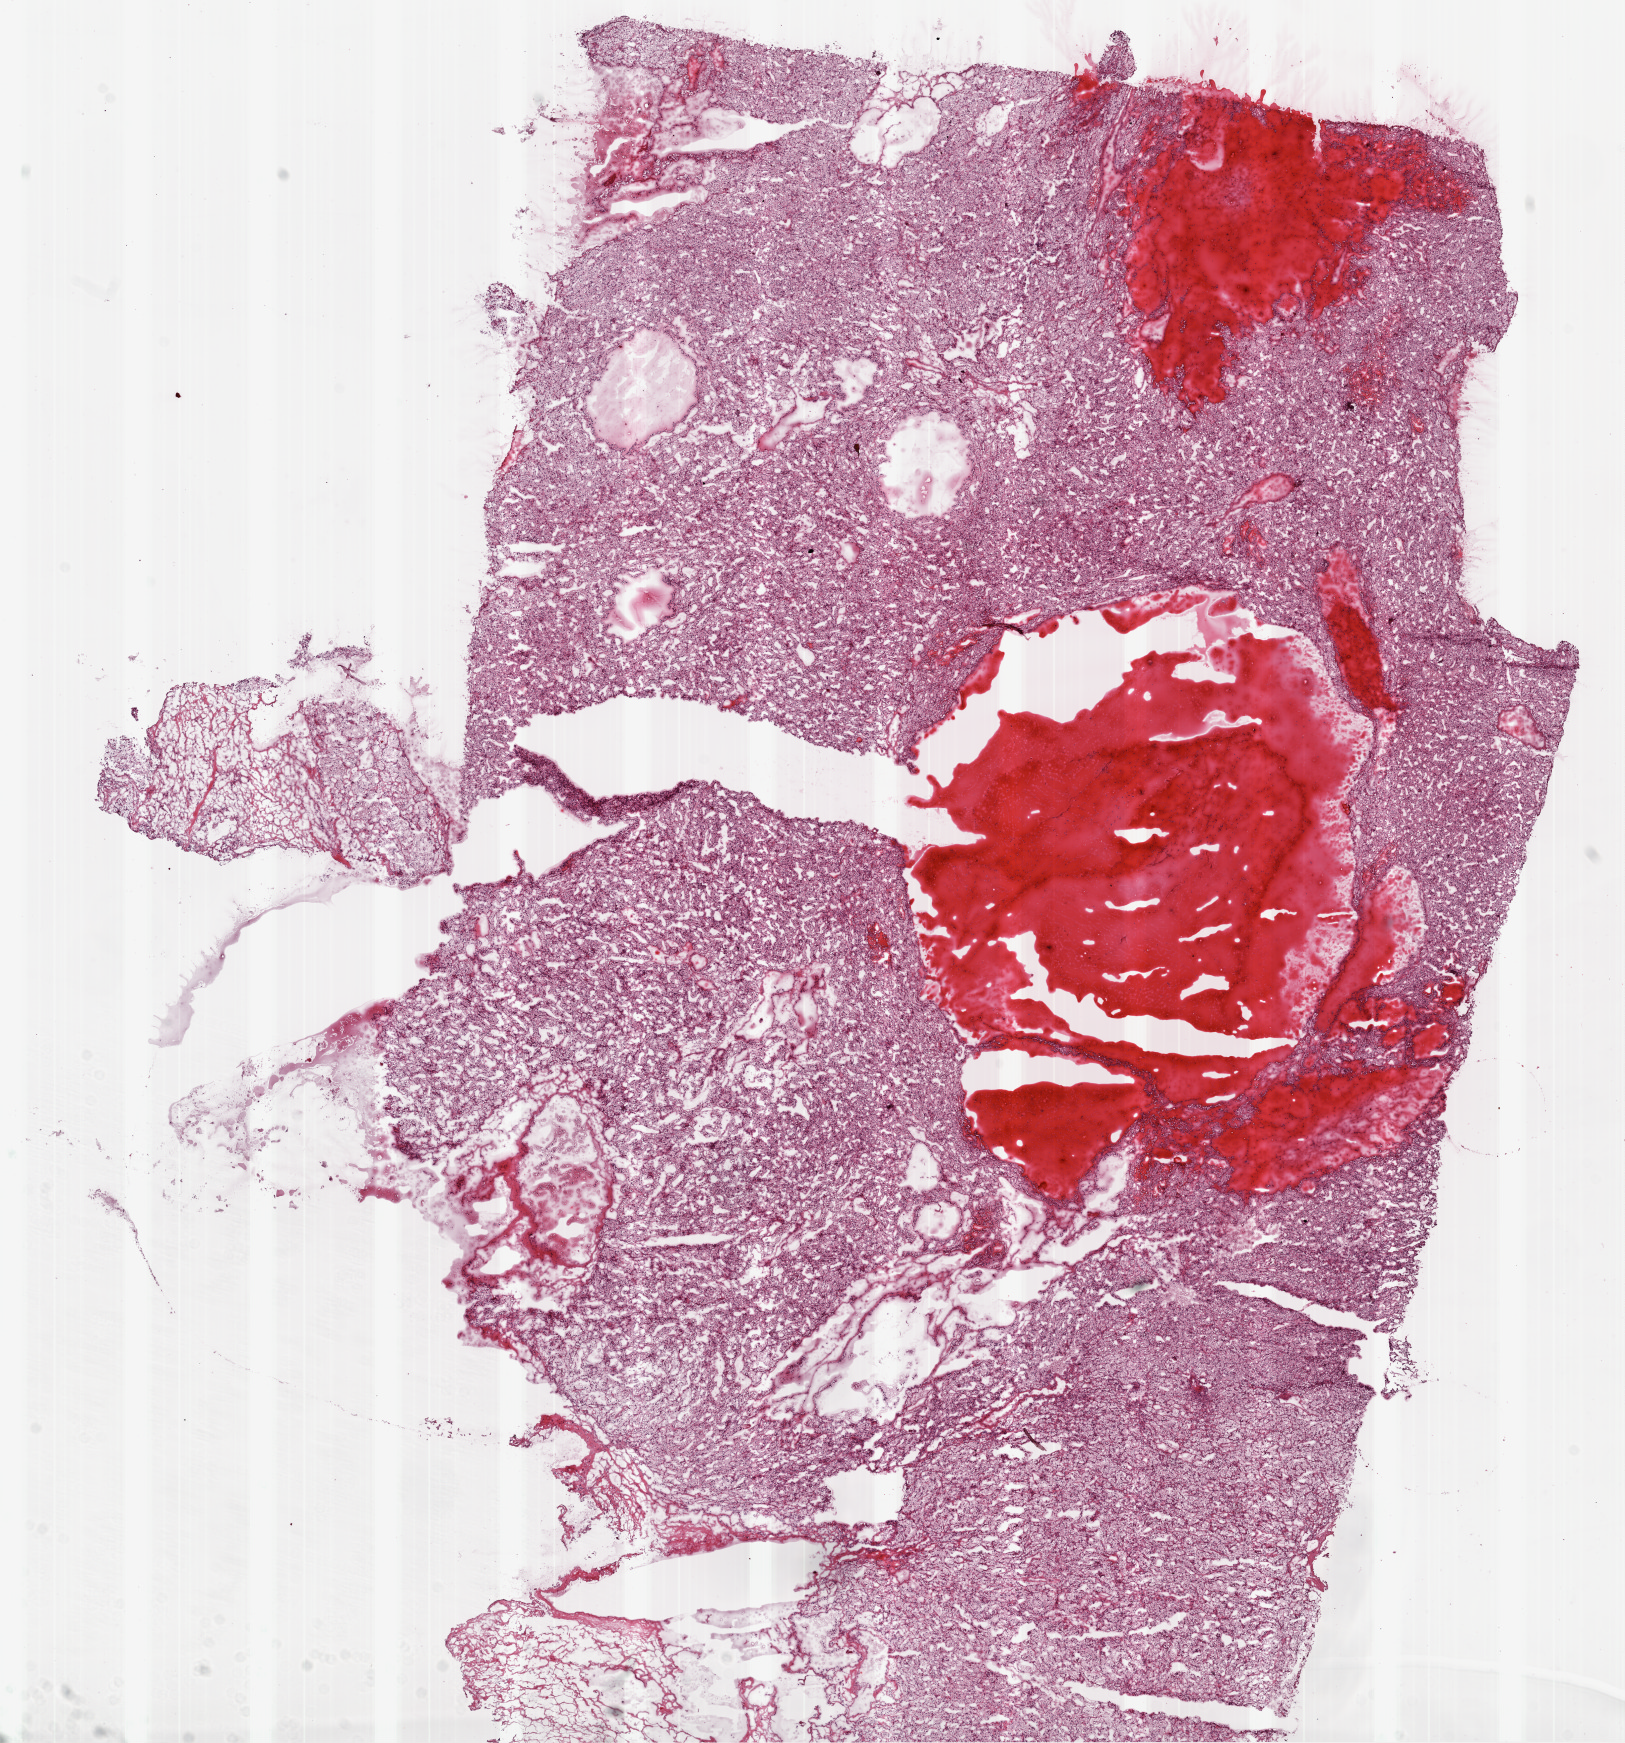
H&E-stained whole-slide image — whole scanned area (about 13.0 x 14.0 mm, slide scanned at 20x) shown as a low-resolution overview. Frozen section from the top of the tissue portion. Primary tumour sample from the kidney. Patient: male, age at initial diagnosis 75 years. Histologic grade: G2 (moderately differentiated). Composition of this section per pathologist review: tumour cells 95%, tumour nuclei 85%, normal cells 0%, stromal cells 5%, necrosis 0%.
- laterality: right
- diagnosis: Clear cell adenocarcinoma, NOS
- TNM: T1a NX M0
- AJCC pathologic stage: I